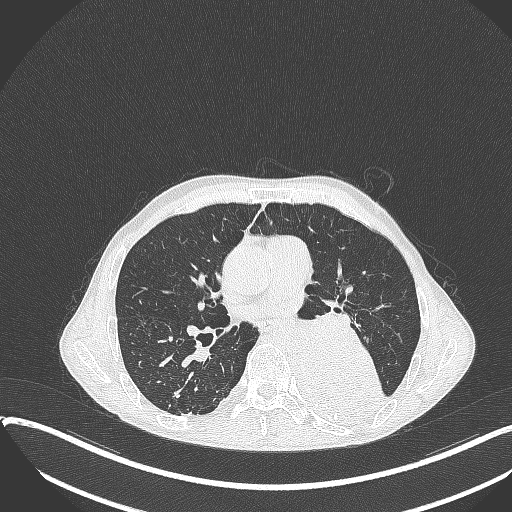
Chest CT, one axial slice. Slice 194 of 401 in the series (ordered by position). 120 kVp. Lung window (W 1500 / L -600 HU). 512 × 512 image matrix, field of view 400 × 400 mm. Male patient, age 57 years. Case-level facts recorded for this patient, not image findings: clinical TNM (as recorded): T4 N0 M0.
Outlined on this slice (bounding box drawn by a radiologist):
- lung tumour (recorded histology: squamous cell carcinoma): box from (x=290, y=331) to (x=383, y=425) px